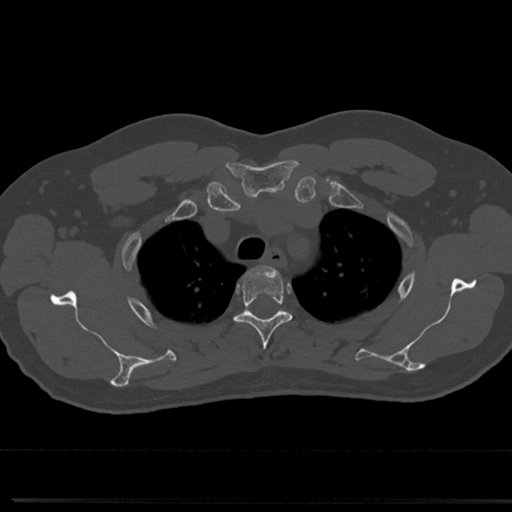
CT including the spine, one axial slice; position 590 of 817 along the scan axis; reconstruction kernel Br40s/3; 120 kVp; bone window (W 1800 / L 400 HU); 0.5 mm slice thickness; 512 × 512 image matrix. Male patient, age 61 years. Case-level facts recorded for this patient, not image findings: primary cancer: prostate.
Outlined on this slice (semi-automatically segmented with operator editing):
- T3 vertebra: bounding box [x1, y1, x2, y2] px = [237, 267, 292, 366]